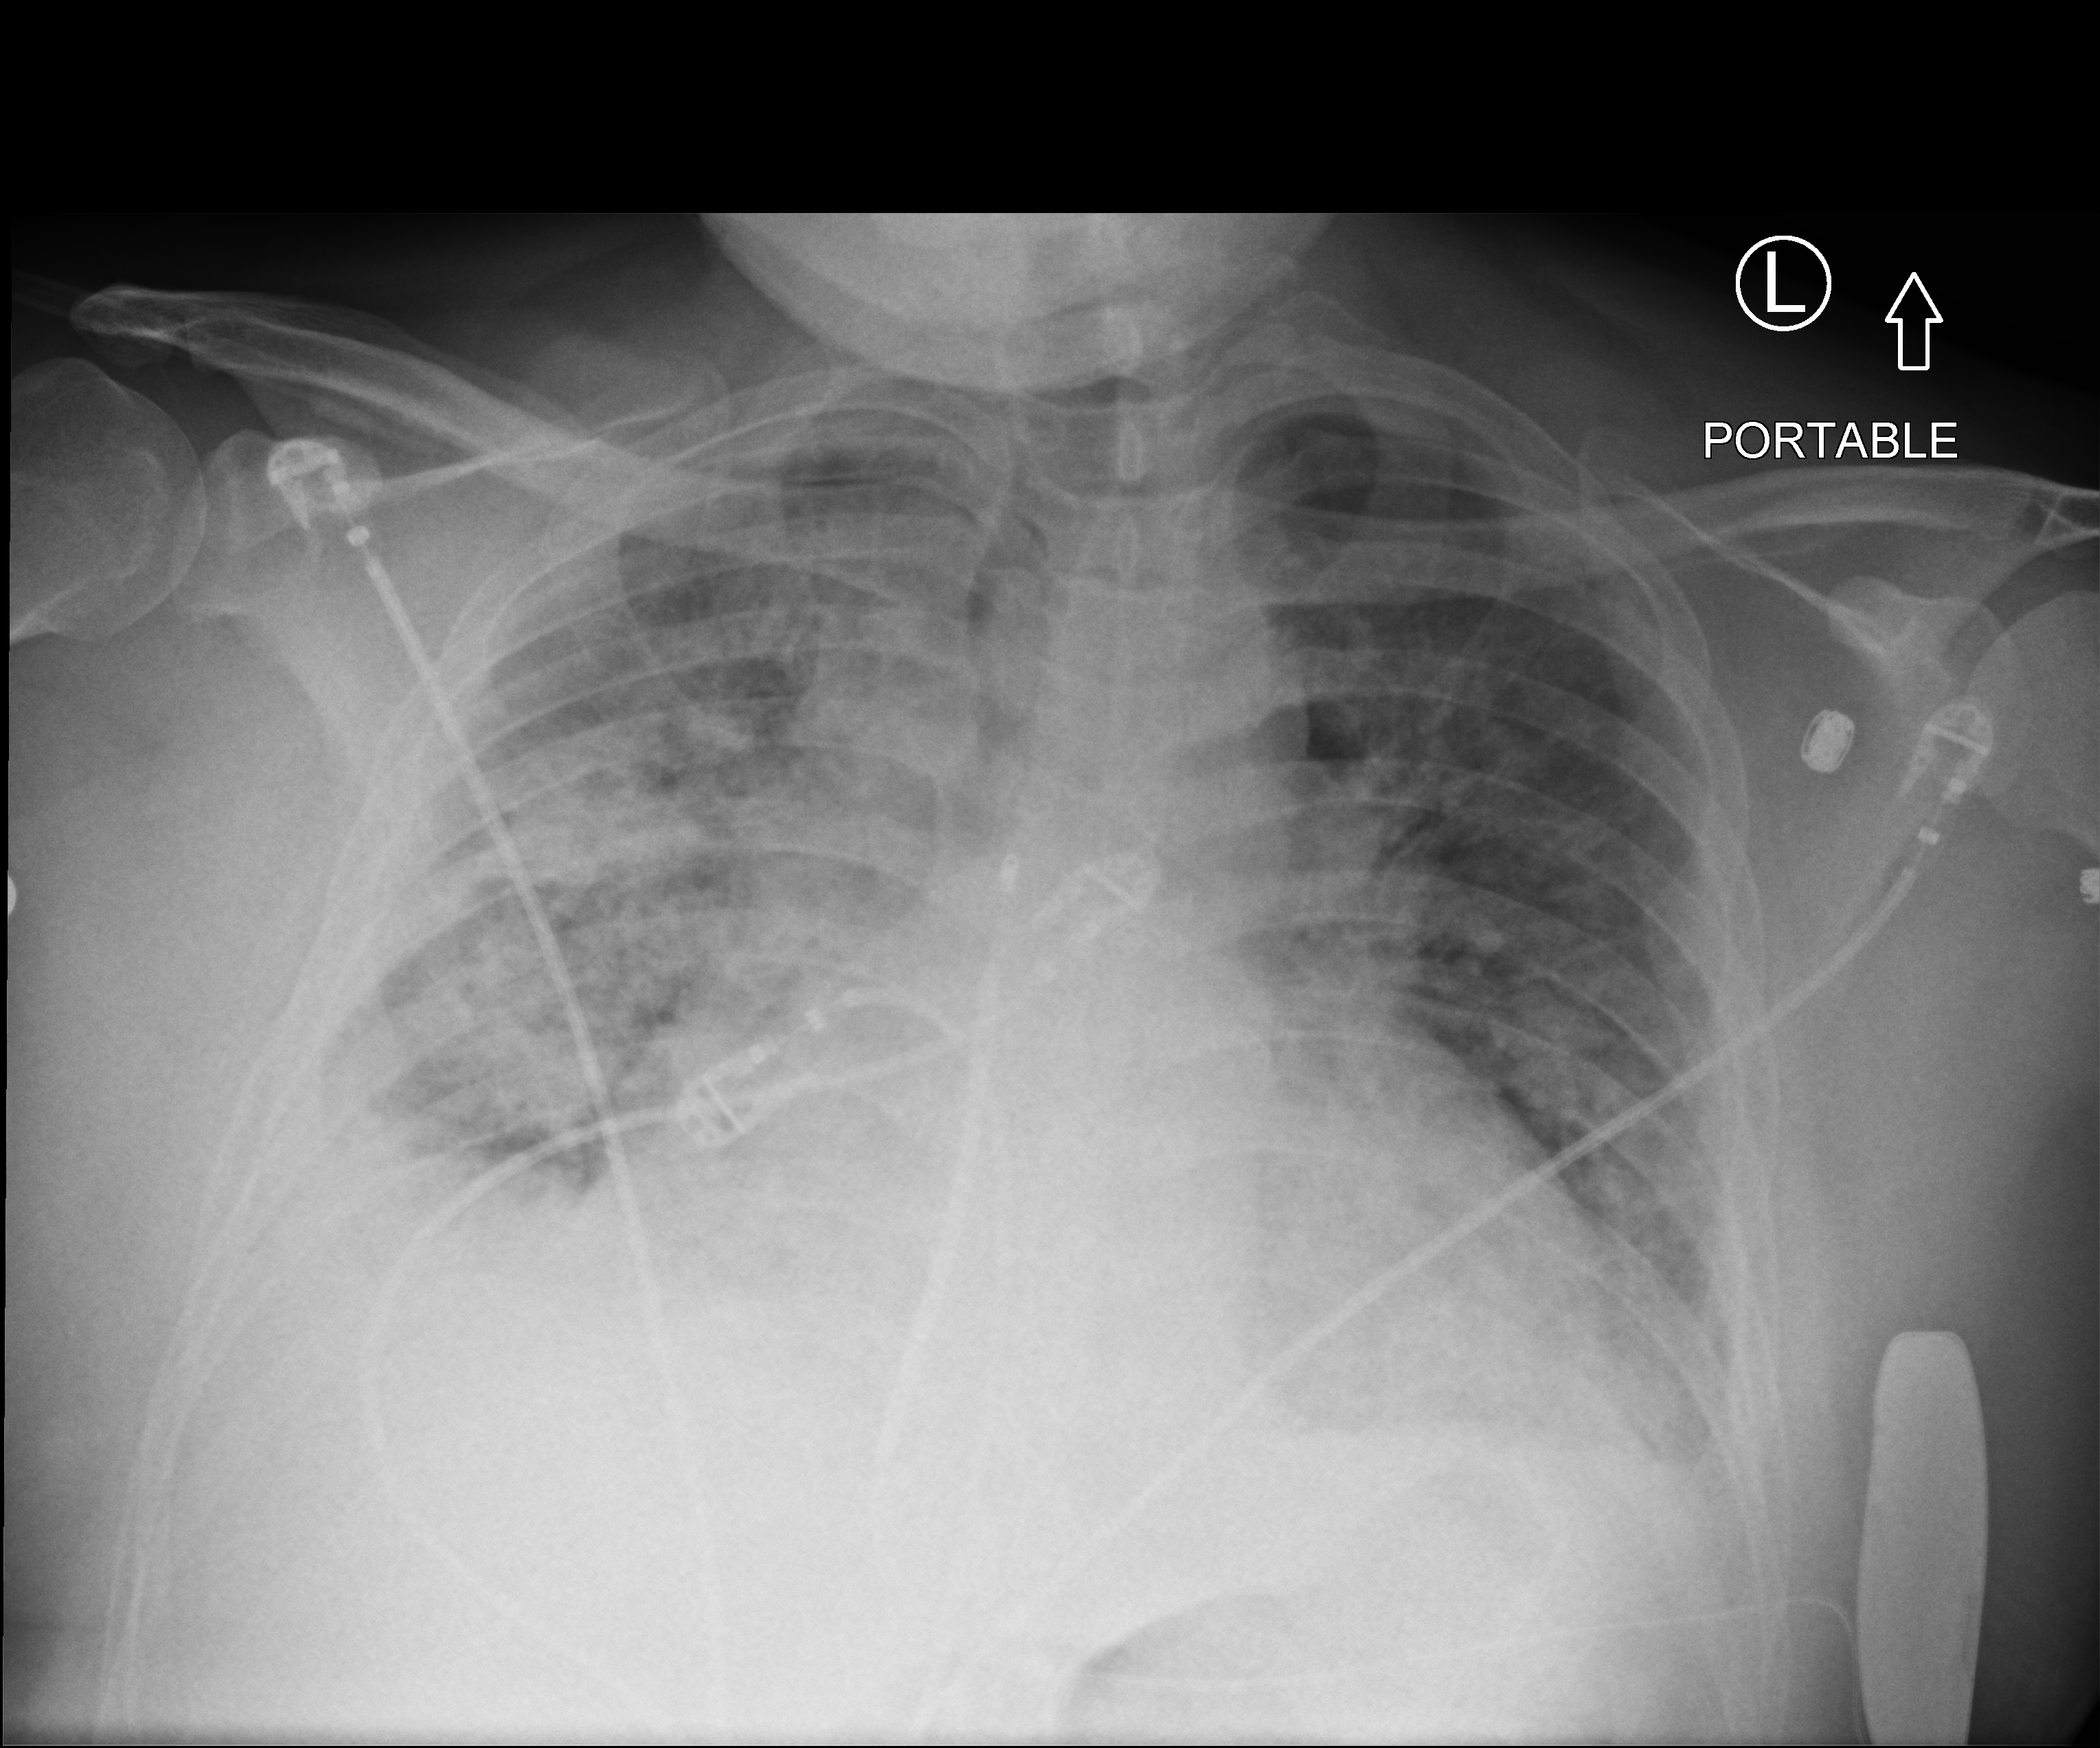
Chest X-ray (portable), anteroposterior (AP) projection. Patient hospitalised with COVID-19; male, aged 18–59 years.
From the hospital-stay record, not from the radiograph (when in the stay this image was taken is not recorded): smoking status (admission record): former; length of hospital stay: 19 days; mechanically ventilated during this hospital stay: no.